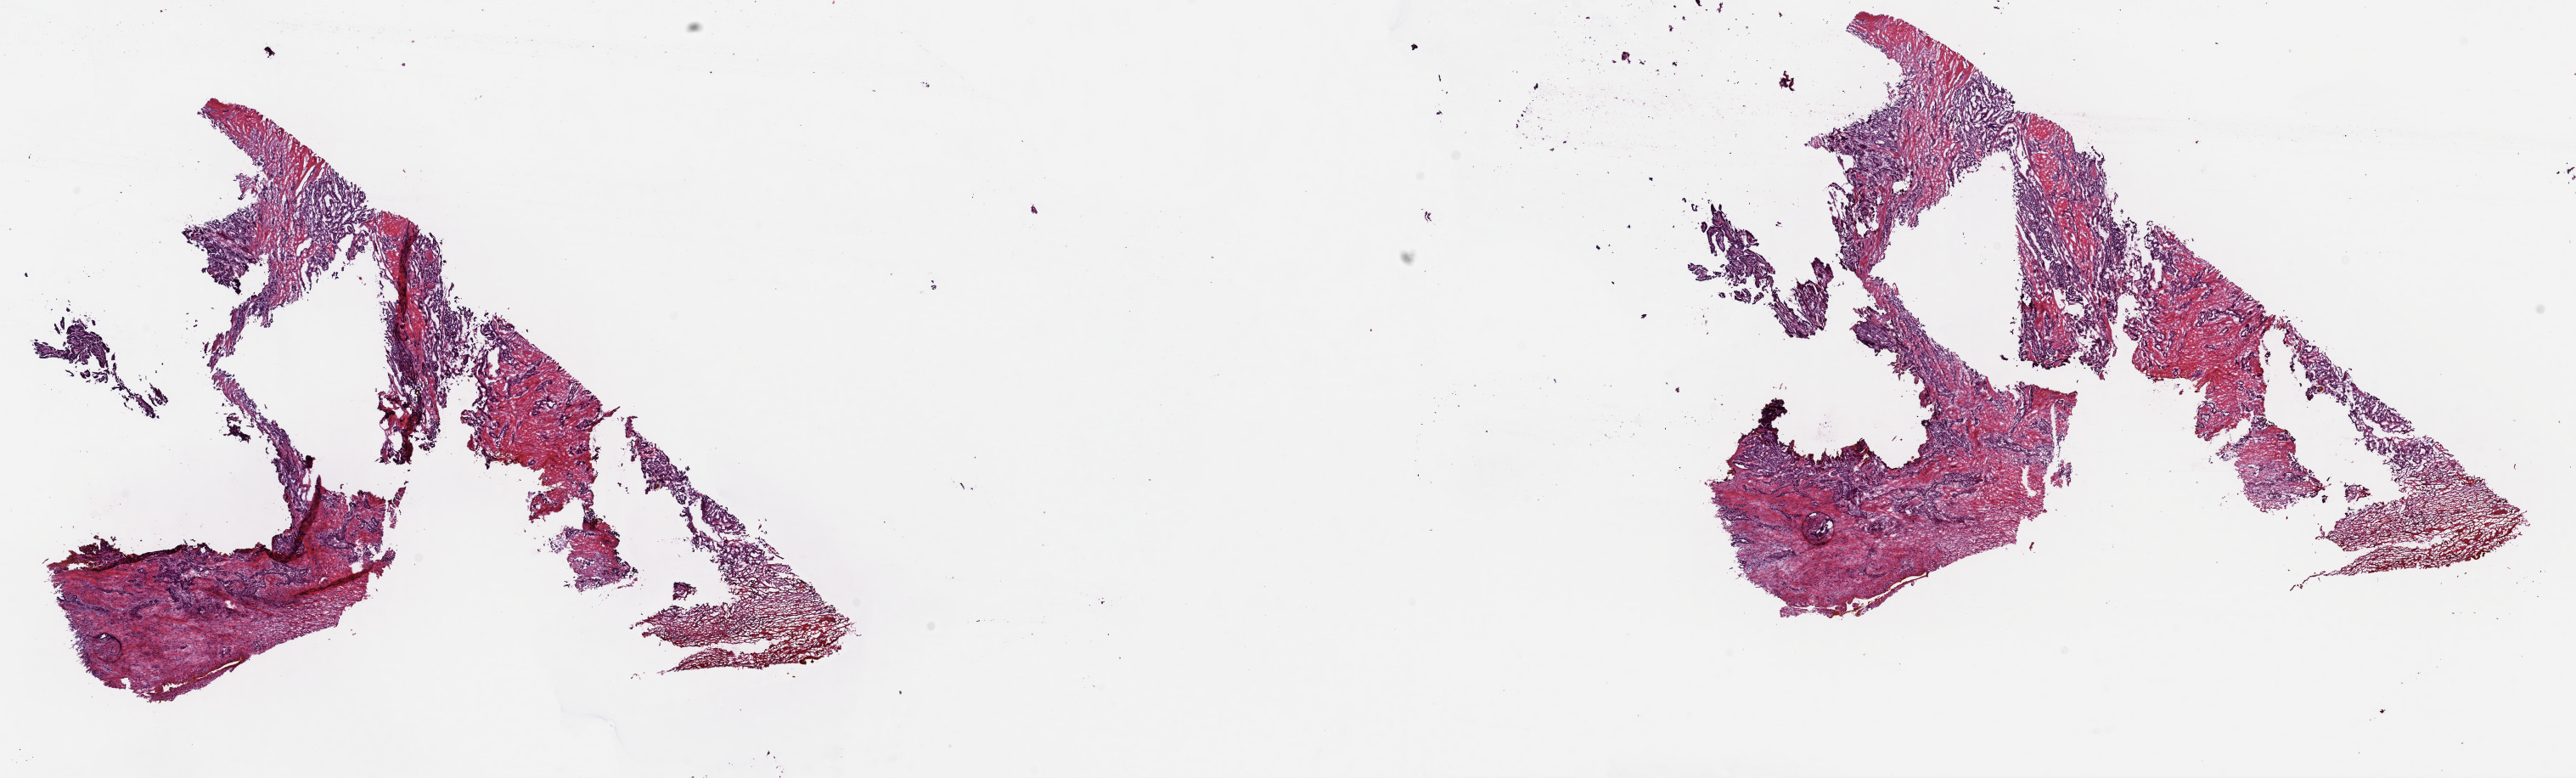
Hematoxylin and eosin (H&E) stained whole-slide image — low-resolution overview of the scanned area, about 24.0 x 7.2 mm (from a 40x scan). Frozen section from the top of the tissue portion. Thyroid, primary tumour sample. Female, age 52 years at initial diagnosis. Composition of this section per pathologist review: tumour cells 90%, tumour nuclei 80%.
Diagnosis: Papillary carcinoma, columnar cell.